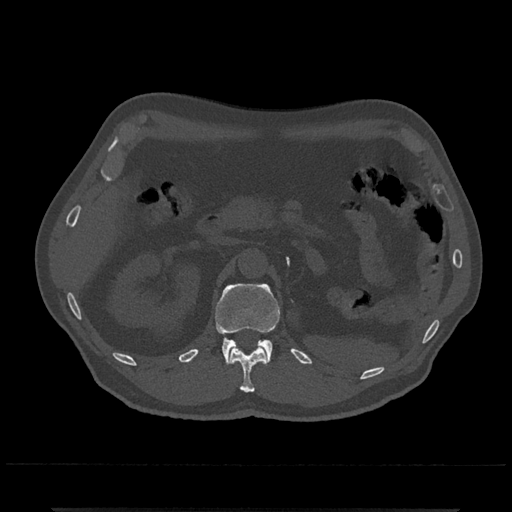
CT including the spine, one axial slice. Position 391 of 797 along the scan axis. Reconstruction kernel Br40s/3. 120 kVp. Bone window (W 1800 / L 400 HU). 512 × 512 image matrix, field of view 393 × 393 mm. Patient: male, 67 years. From the clinical record (not read from this slice): primary cancer: prostate.
Annotated regions visible in this slice (semi-automatically segmented with operator editing):
- L1 vertebra: box from (x=215, y=283) to (x=280, y=364) px
- T12 vertebra: (x=230, y=346)–(x=267, y=393)